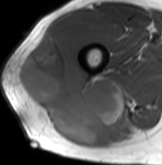
MRI of an extremity soft-tissue mass, one axial slice. Position 55 of 61 along the scan axis. MR volume resampled by the dataset authors to the PET/CT grid (not the native acquisition matrix). 3.27 mm slice thickness. 162 × 165 image matrix, field of view 158 × 161 mm. Male patient. Case-level facts recorded for this patient, not image findings: histological type: poorly differentiated synovial sarcoma; grade: high; site of the primary tumour: right buttock.
Outlined on this slice (expert contour drawn on MRI and transferred to this co-registered scan by the dataset authors):
- gross tumour volume including surrounding oedema: bounding box [x1, y1, x2, y2] px = [16, 33, 138, 146]
- gross tumour volume (mass): [16, 33, 124, 146]